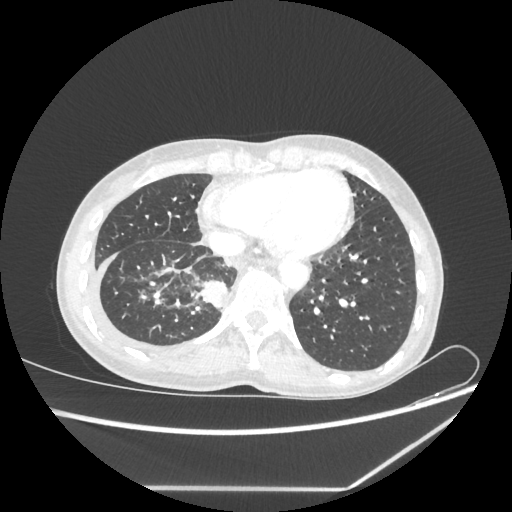
Chest CT, one axial slice. Position 68 of 237 along the scan axis. Reconstruction kernel STANDARD. 80 kVp. Lung window (W 1500 / L -600 HU). 1.25 mm slice thickness. 512 × 512 image matrix. Patient: female, 59 years. Case-level facts recorded for this patient, not image findings: clinical TNM (as recorded): T1c N1 M1.
Annotated regions visible in this slice (bounding box drawn by a radiologist):
- lung tumour (recorded histology: adenocarcinoma): bounding box <201,277,229,312> (left, top, right, bottom; pixels)